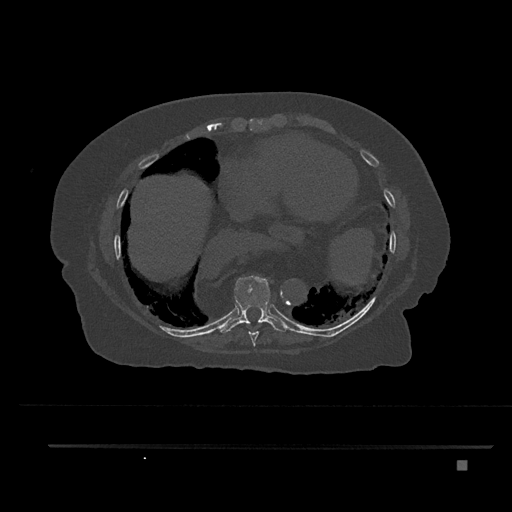
CT including the spine, one axial slice. Bone window (W 1800 / L 400 HU). 0.5 mm slice thickness. 512 × 512 image matrix, field of view 437 × 437 mm. Female patient, age 76 years. Case-level facts recorded for this patient, not image findings: primary cancer: lung.
Outlined on this slice (semi-automatically segmented with operator editing):
- T8 vertebra: bounding box <248,331,259,347> (left, top, right, bottom; pixels)
- T9 vertebra: <219,275,289,333>